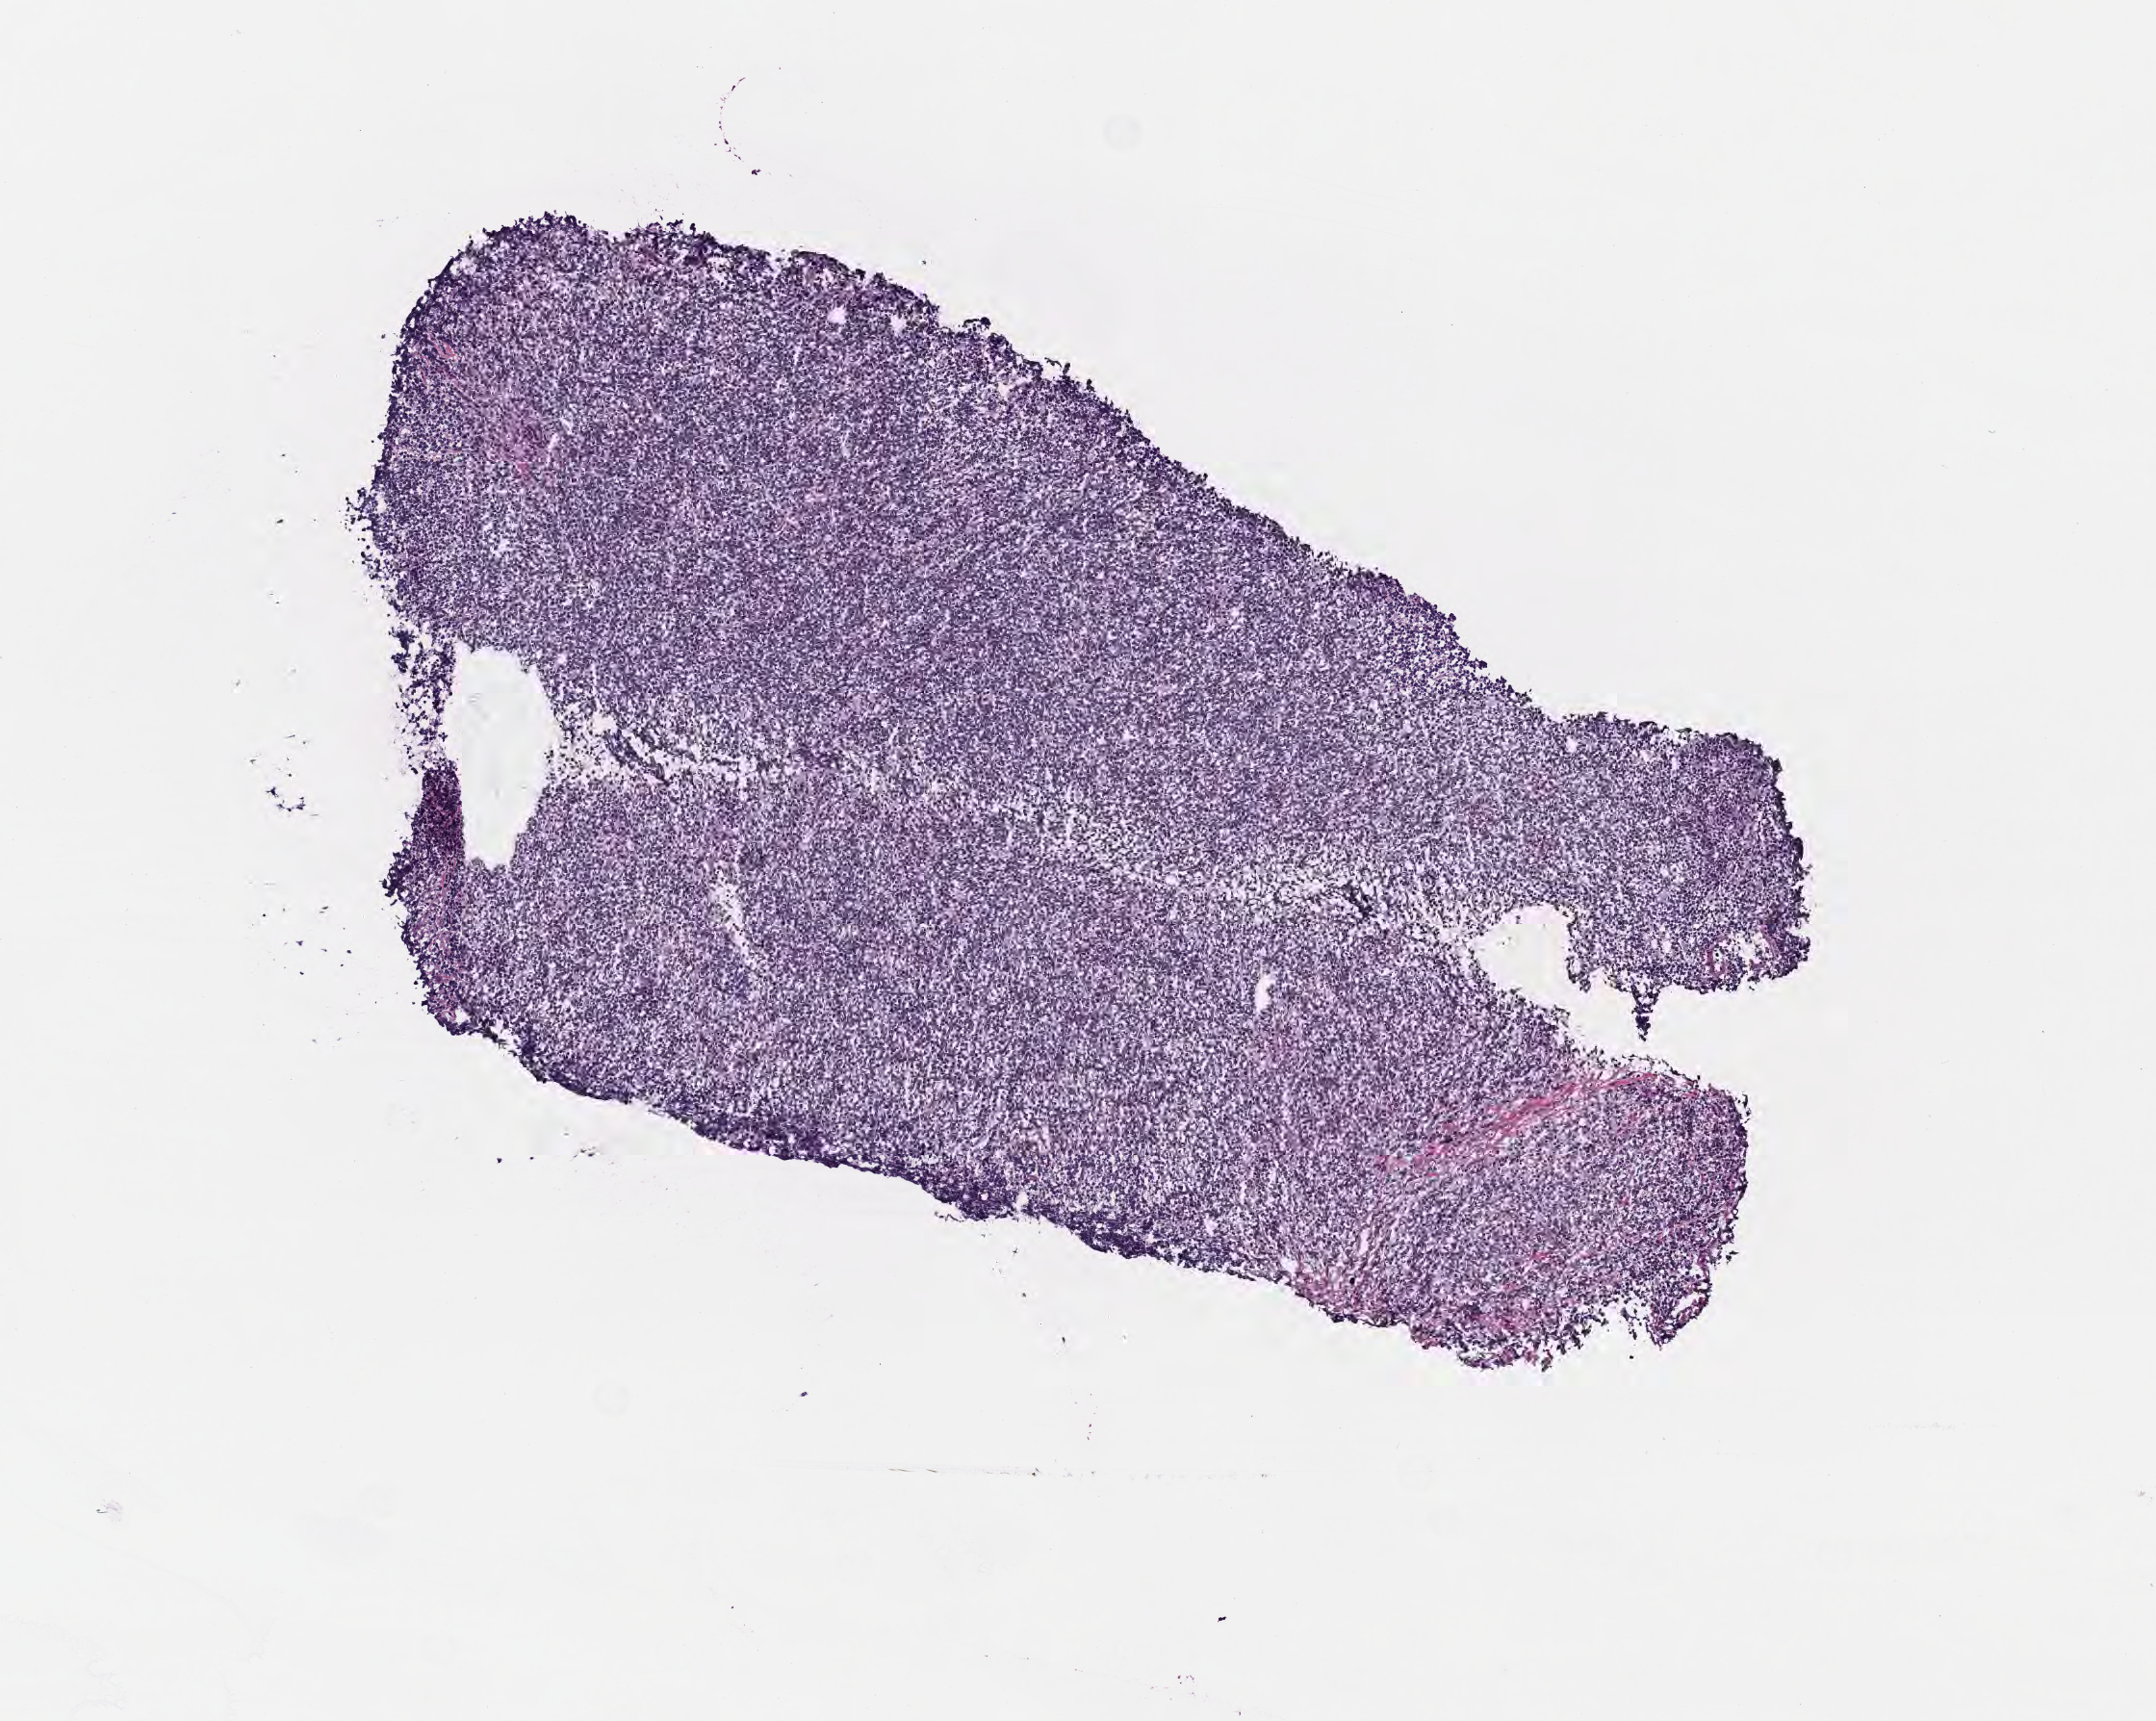
Digitized hematoxylin and eosin (H&E)-stained section — shown as a low-resolution overview of the whole scanned area (about 4.5 x 3.6 mm); cryosection; specimen: primary tumor; anatomic site: cranium. Patient: female, age at initial diagnosis 1 years. Slide review estimates, as recorded: tumor cells 95%, tumor nuclei 95%, stromal cells 2%, necrosis 3%, normal cells 0%. Infiltration values recorded for this section: lymphocyte infiltration 10%, monocyte infiltration 25%, neutrophil infiltration 10%.
Histologic diagnosis: Burkitt lymphoma, NOS. Ann Arbor stage (patient): Stage III. Section: top of the tissue portion.